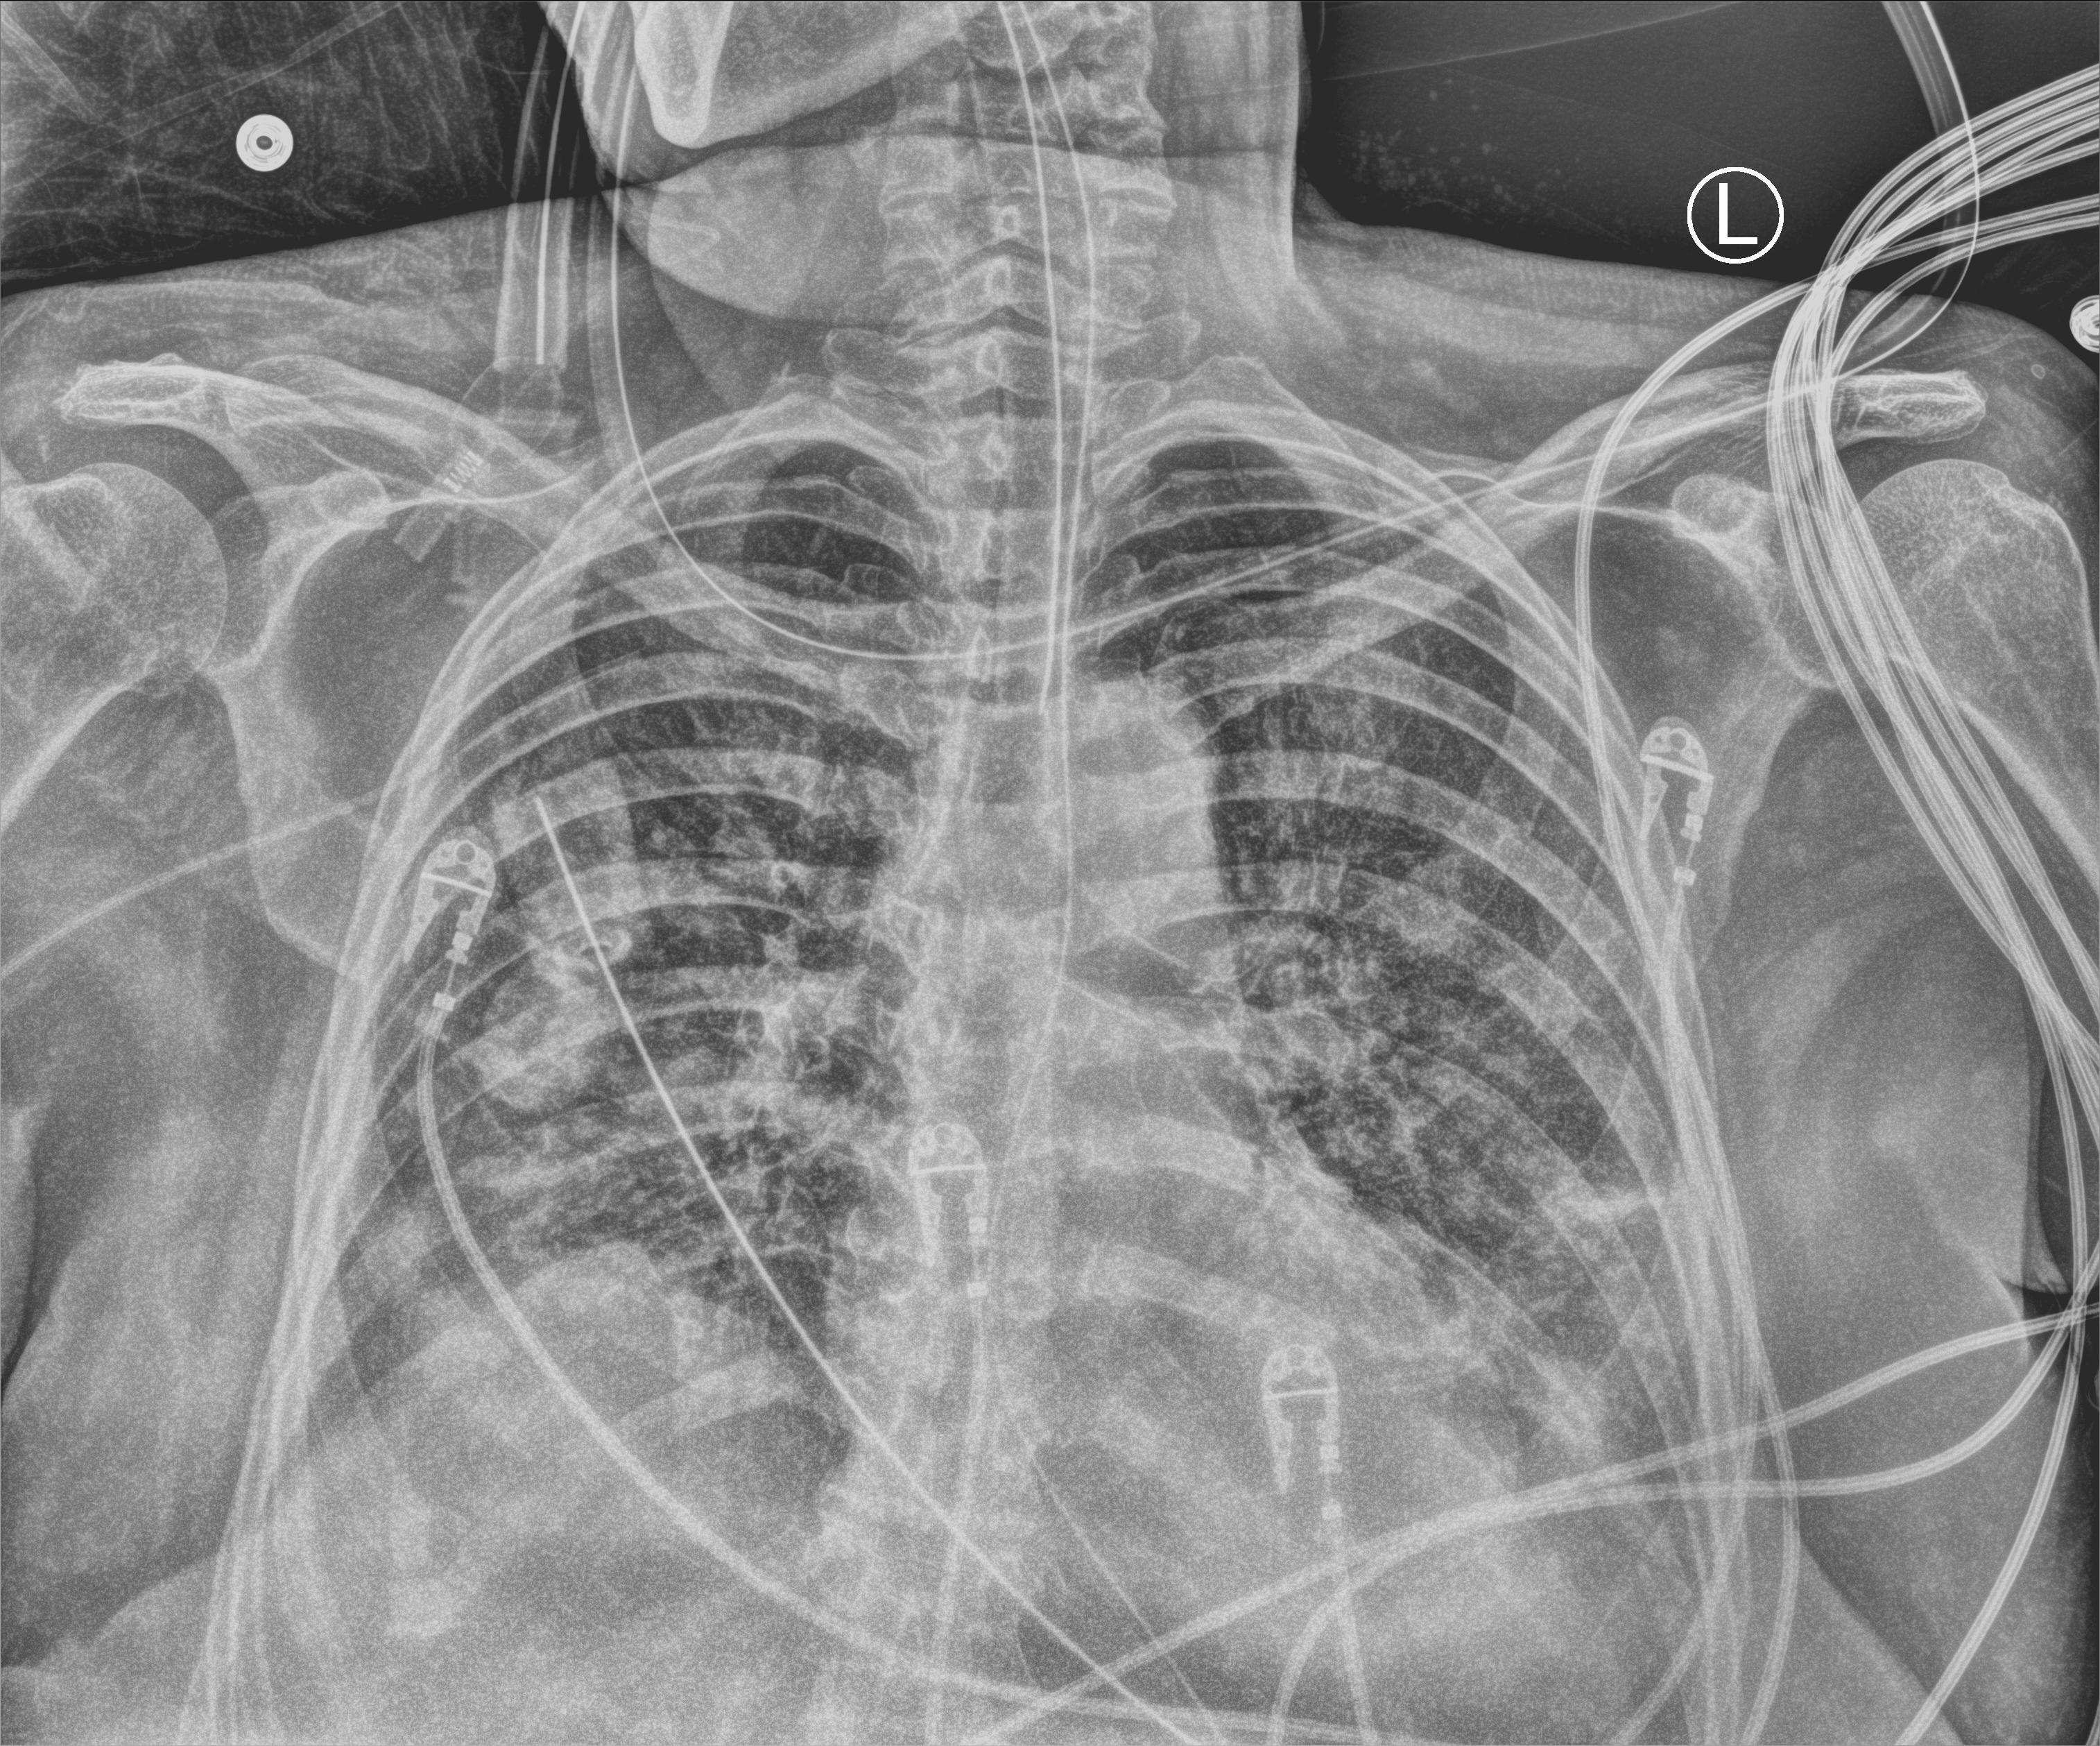
Chest X-ray (portable); anteroposterior (AP) projection. Female patient hospitalised with COVID-19, age 75–90 years.
Hospital-stay facts (about this admission, not read from this image; timing relative to this image not recorded): admitted to intensive care during this hospital stay: yes; smoking status (admission record): never; COPD (admission record): no.